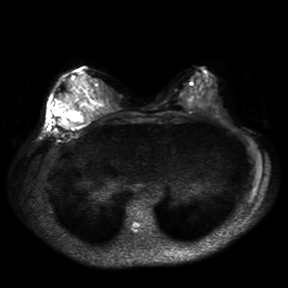
Breast MRI, one axial slice; slice 14 of 30 in the series (ordered by position); diffusion-weighted series; image 2 of 4 stored at this slice position (different b-values; order by instance number); 3 T; 288 × 288 image matrix, field of view 360 × 360 mm. Female patient.
Outlined on this slice (expert manual segmentation):
- tumour on diffusion-weighted imaging: bounding box <52,104,74,128> (left, top, right, bottom; pixels)